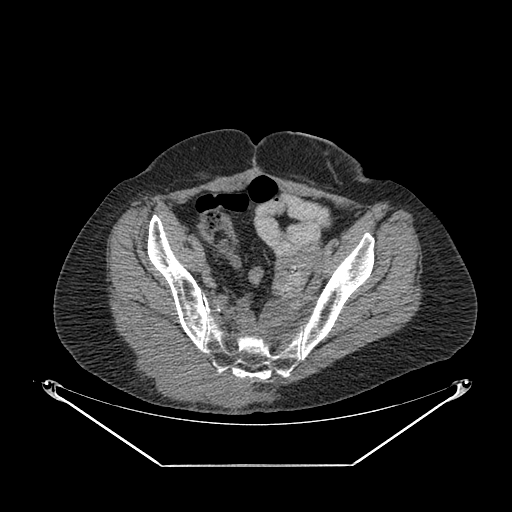
CT of an extremity soft-tissue mass (from a PET/CT study), one axial slice; position 68 of 267 along the scan axis; reconstruction kernel SOFT; 140 kVp; soft-tissue window (W 400 / L 40 HU); 3.75 mm slice thickness; 512 × 512 image matrix, field of view 500 × 500 mm. Female patient. From the clinical record (not read from this slice): histological type: spindle cell suggestive of myxofibrosarcoma; grade: intermediate; site of the primary tumour: right buttock.
Outlined on this slice (expert contour drawn on MRI and transferred to this co-registered scan by the dataset authors):
- gross tumour volume (mass): bounding box <126,333,250,407> (left, top, right, bottom; pixels)